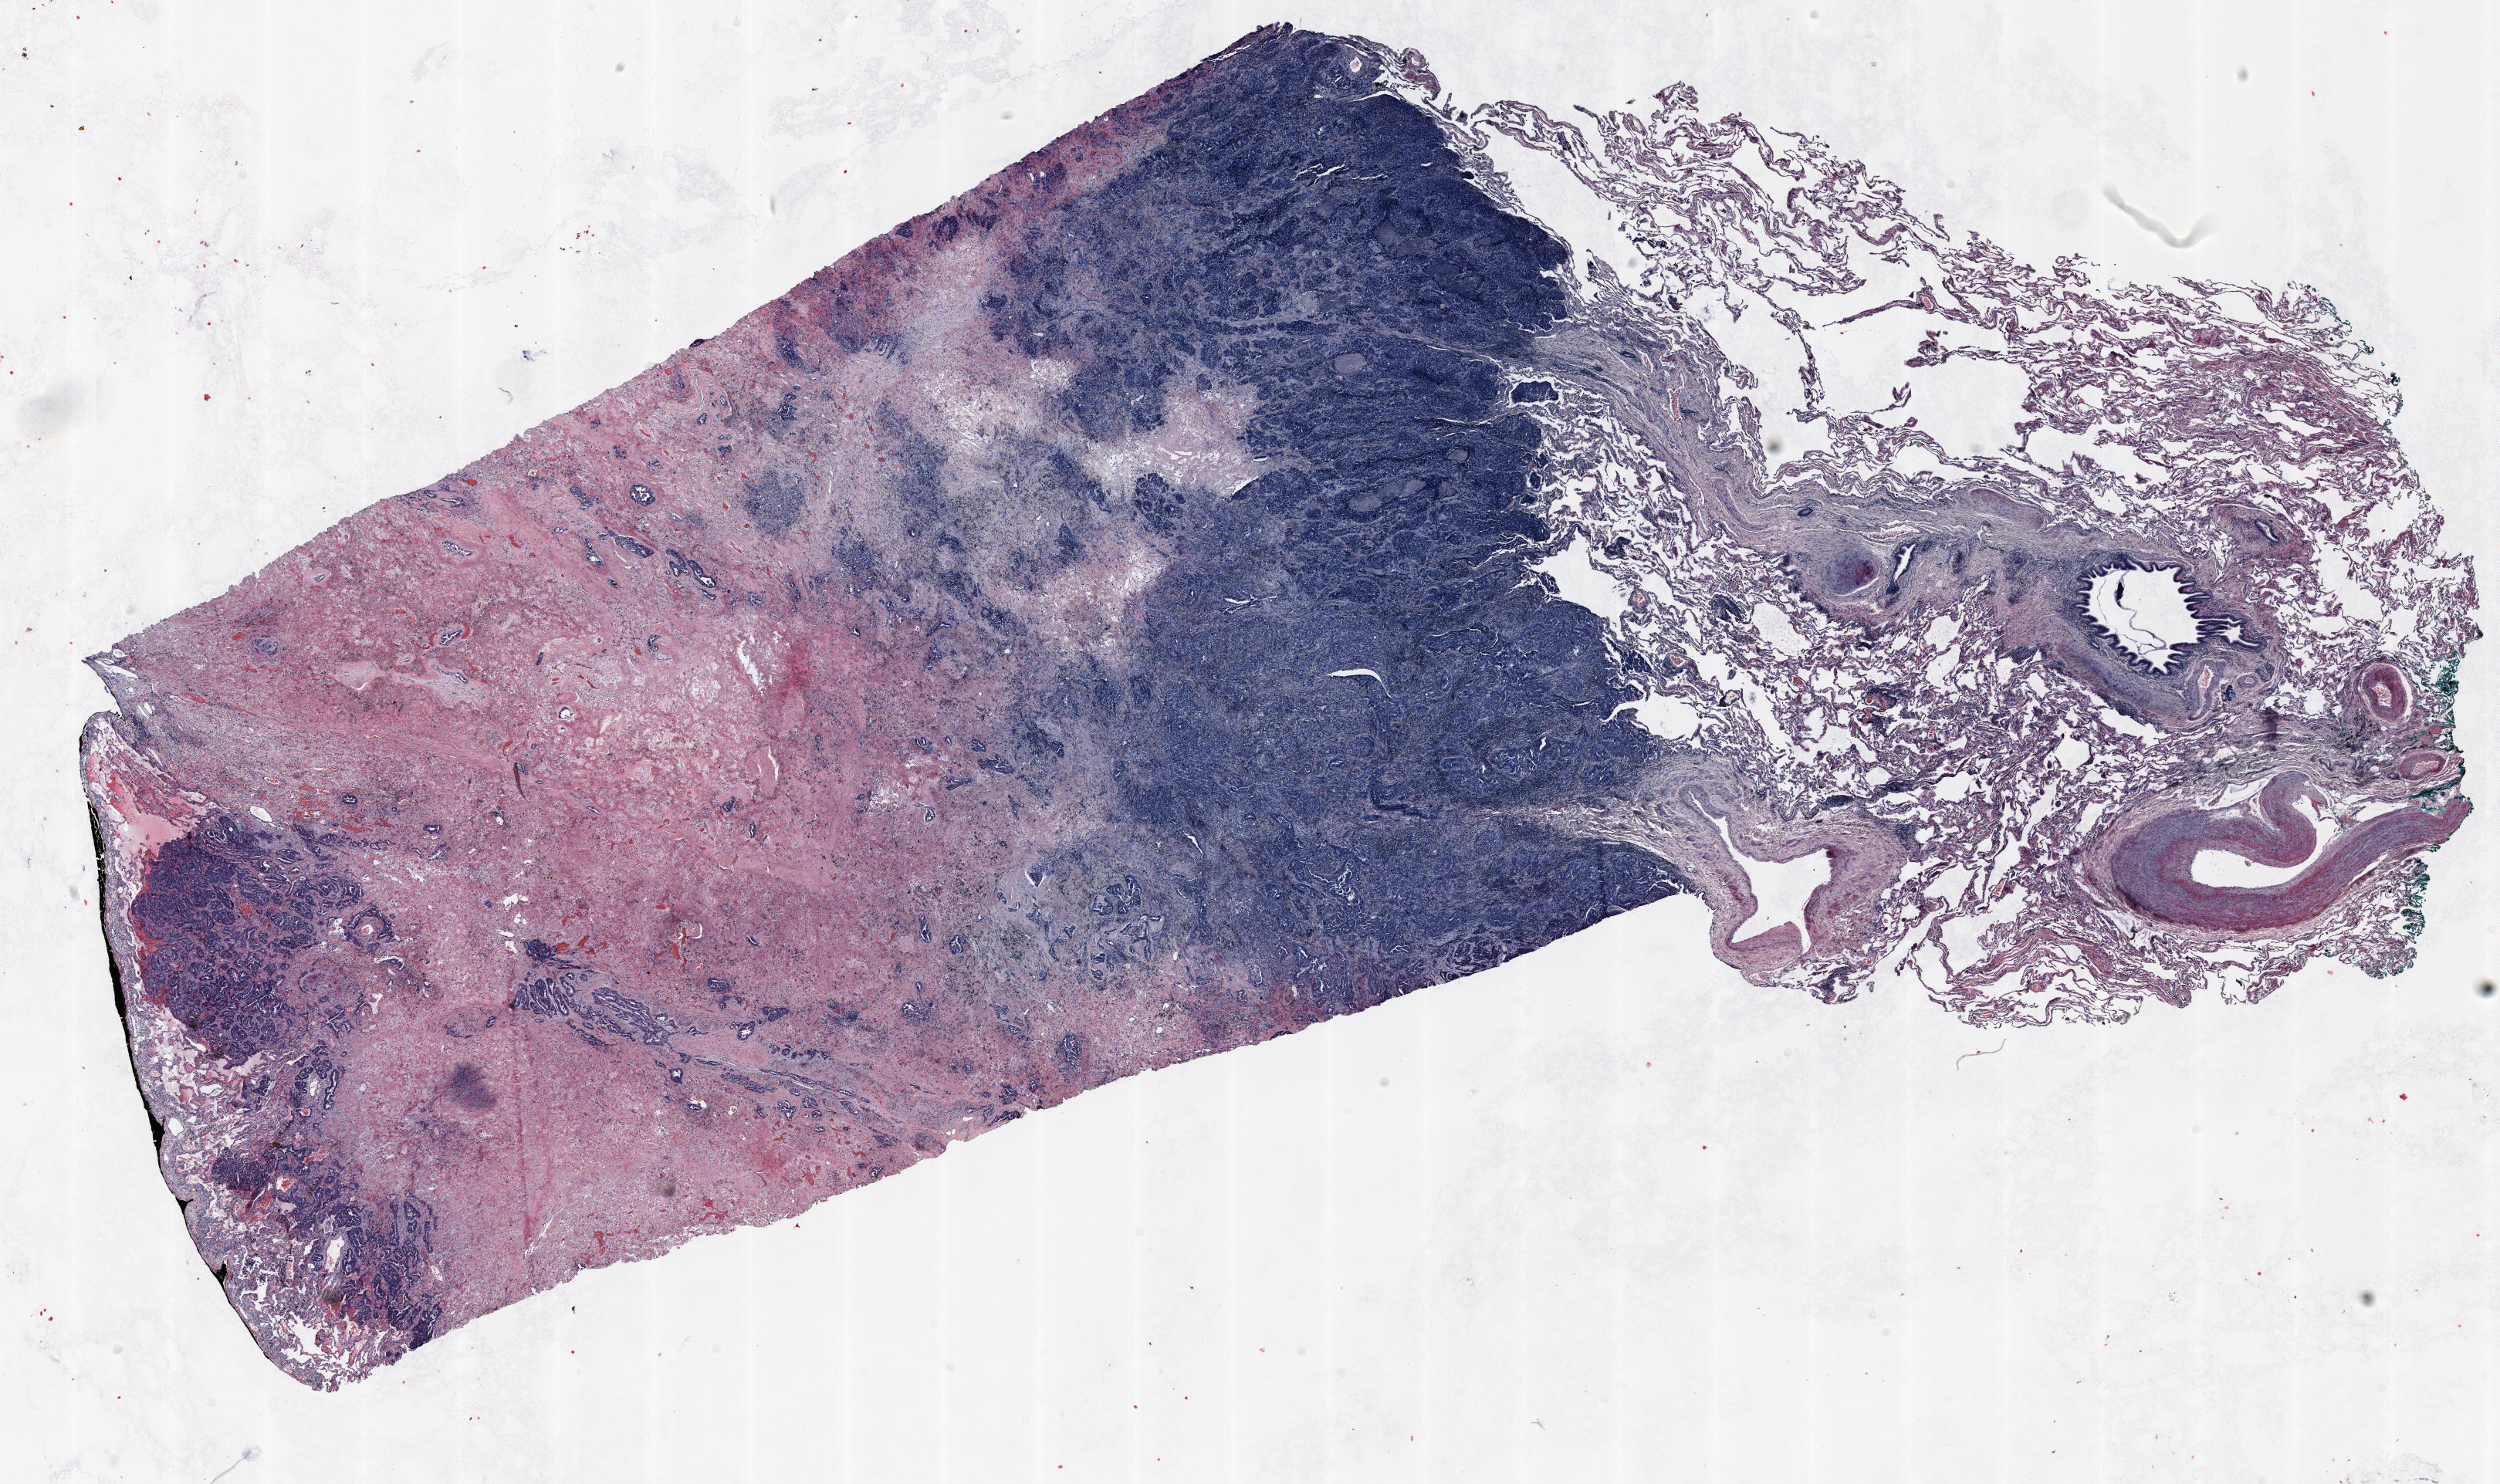
Whole-slide histology image, H&E — shown as a low-resolution overview of the whole scanned area (about 26.0 x 15.5 mm), FFPE section, lung. Female, age 66 at enrolment. Former smoker at enrolment. Grade: poorly differentiated (G3).
* stage (AJCC 6th edition): IB
* primary tumour location (clinical record): left upper lobe
* ICD-O-3 topography: upper lobe of lung (C34.1)
* participant's lung-cancer diagnosis: Adenocarcinoma, NOS (ICD-O-3 8140/3)
* tumour size (pathology): 40 mm